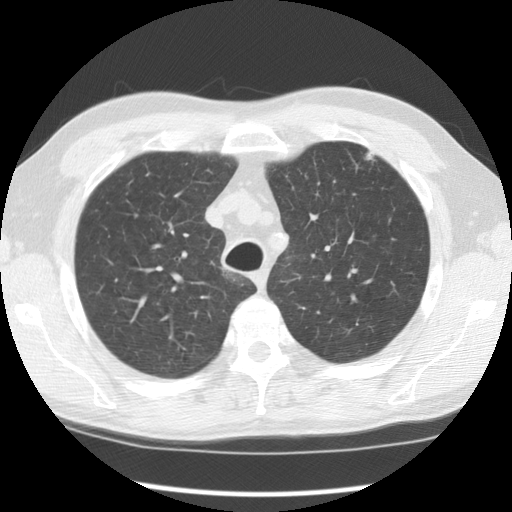
Low-dose screening chest CT, axial slice. Baseline screening round. Lung window (W 1500 / L -600 HU). 2.5 mm slice thickness. Standard (soft-tissue) reconstruction kernel (STANDARD). 120 kVp. Slice 28 of 121 in the series. Male participant, aged 55 years at enrolment.
- Expert reader's lesion annotation, bounding box <349,137,389,178> (left, top, right, bottom; pixels).
- Screening reader's record for this exam (one nodule recorded; not confirmed to be the boxed lesion): non-calcified nodule or mass ≥4 mm, left upper lobe, 5 × 5 mm, poorly defined margins, soft tissue attenuation.
- Lung cancer was diagnosed 159 days after this screen: adenocarcinoma, NOS, left upper lobe, moderately differentiated (G2), stage IA (AJCC 6th edition), 8 mm at pathology.